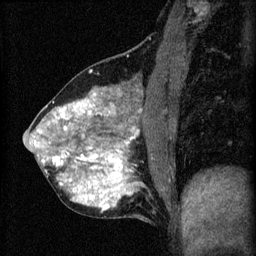
Breast MRI (dynamic contrast-enhanced), one sagittal slice; slice 26 of 60 in the series (ordered by position); 3 images stored at this slice position (order not interpretable as contrast timing); 1.5 T; TE 4.2 ms, TR 8.2 ms; 2 mm slice thickness; 256 × 256 image matrix. Patient: female, 40 years.
Structures marked on this image (semi-automatically segmented with operator editing):
- analysis volume of interest (the breast-tissue region the enhancement analysis was run in; not a lesion): bounding box <24,76,175,219> (left, top, right, bottom; pixels)
- tumour enhancement mask (voxels above the 70 % enhancement threshold inside the analysis volume of interest): <34,92,139,211>